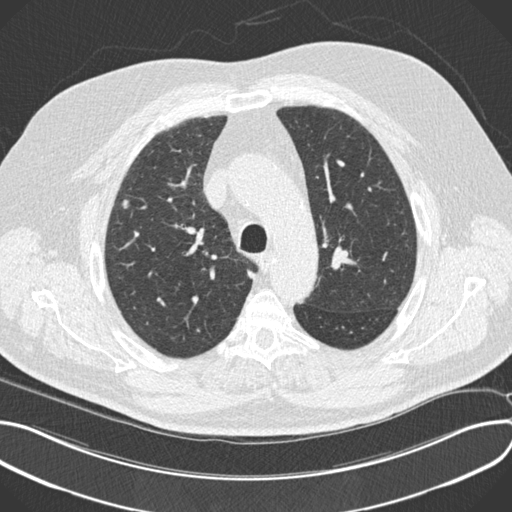
Low-dose screening chest CT, one axial slice. Slice 157 of 212 in the series (ordered by position). Reconstruction kernel B30f. 120 kVp. Lung window (W 1500 / L -600 HU). 2 mm slice thickness. 512 × 512 image matrix.
Structures marked on this image (manually delineated by an expert):
- lesion 1 (tumor, upper lobe of right lung): bounding box <123,199,129,209> (left, top, right, bottom; pixels)